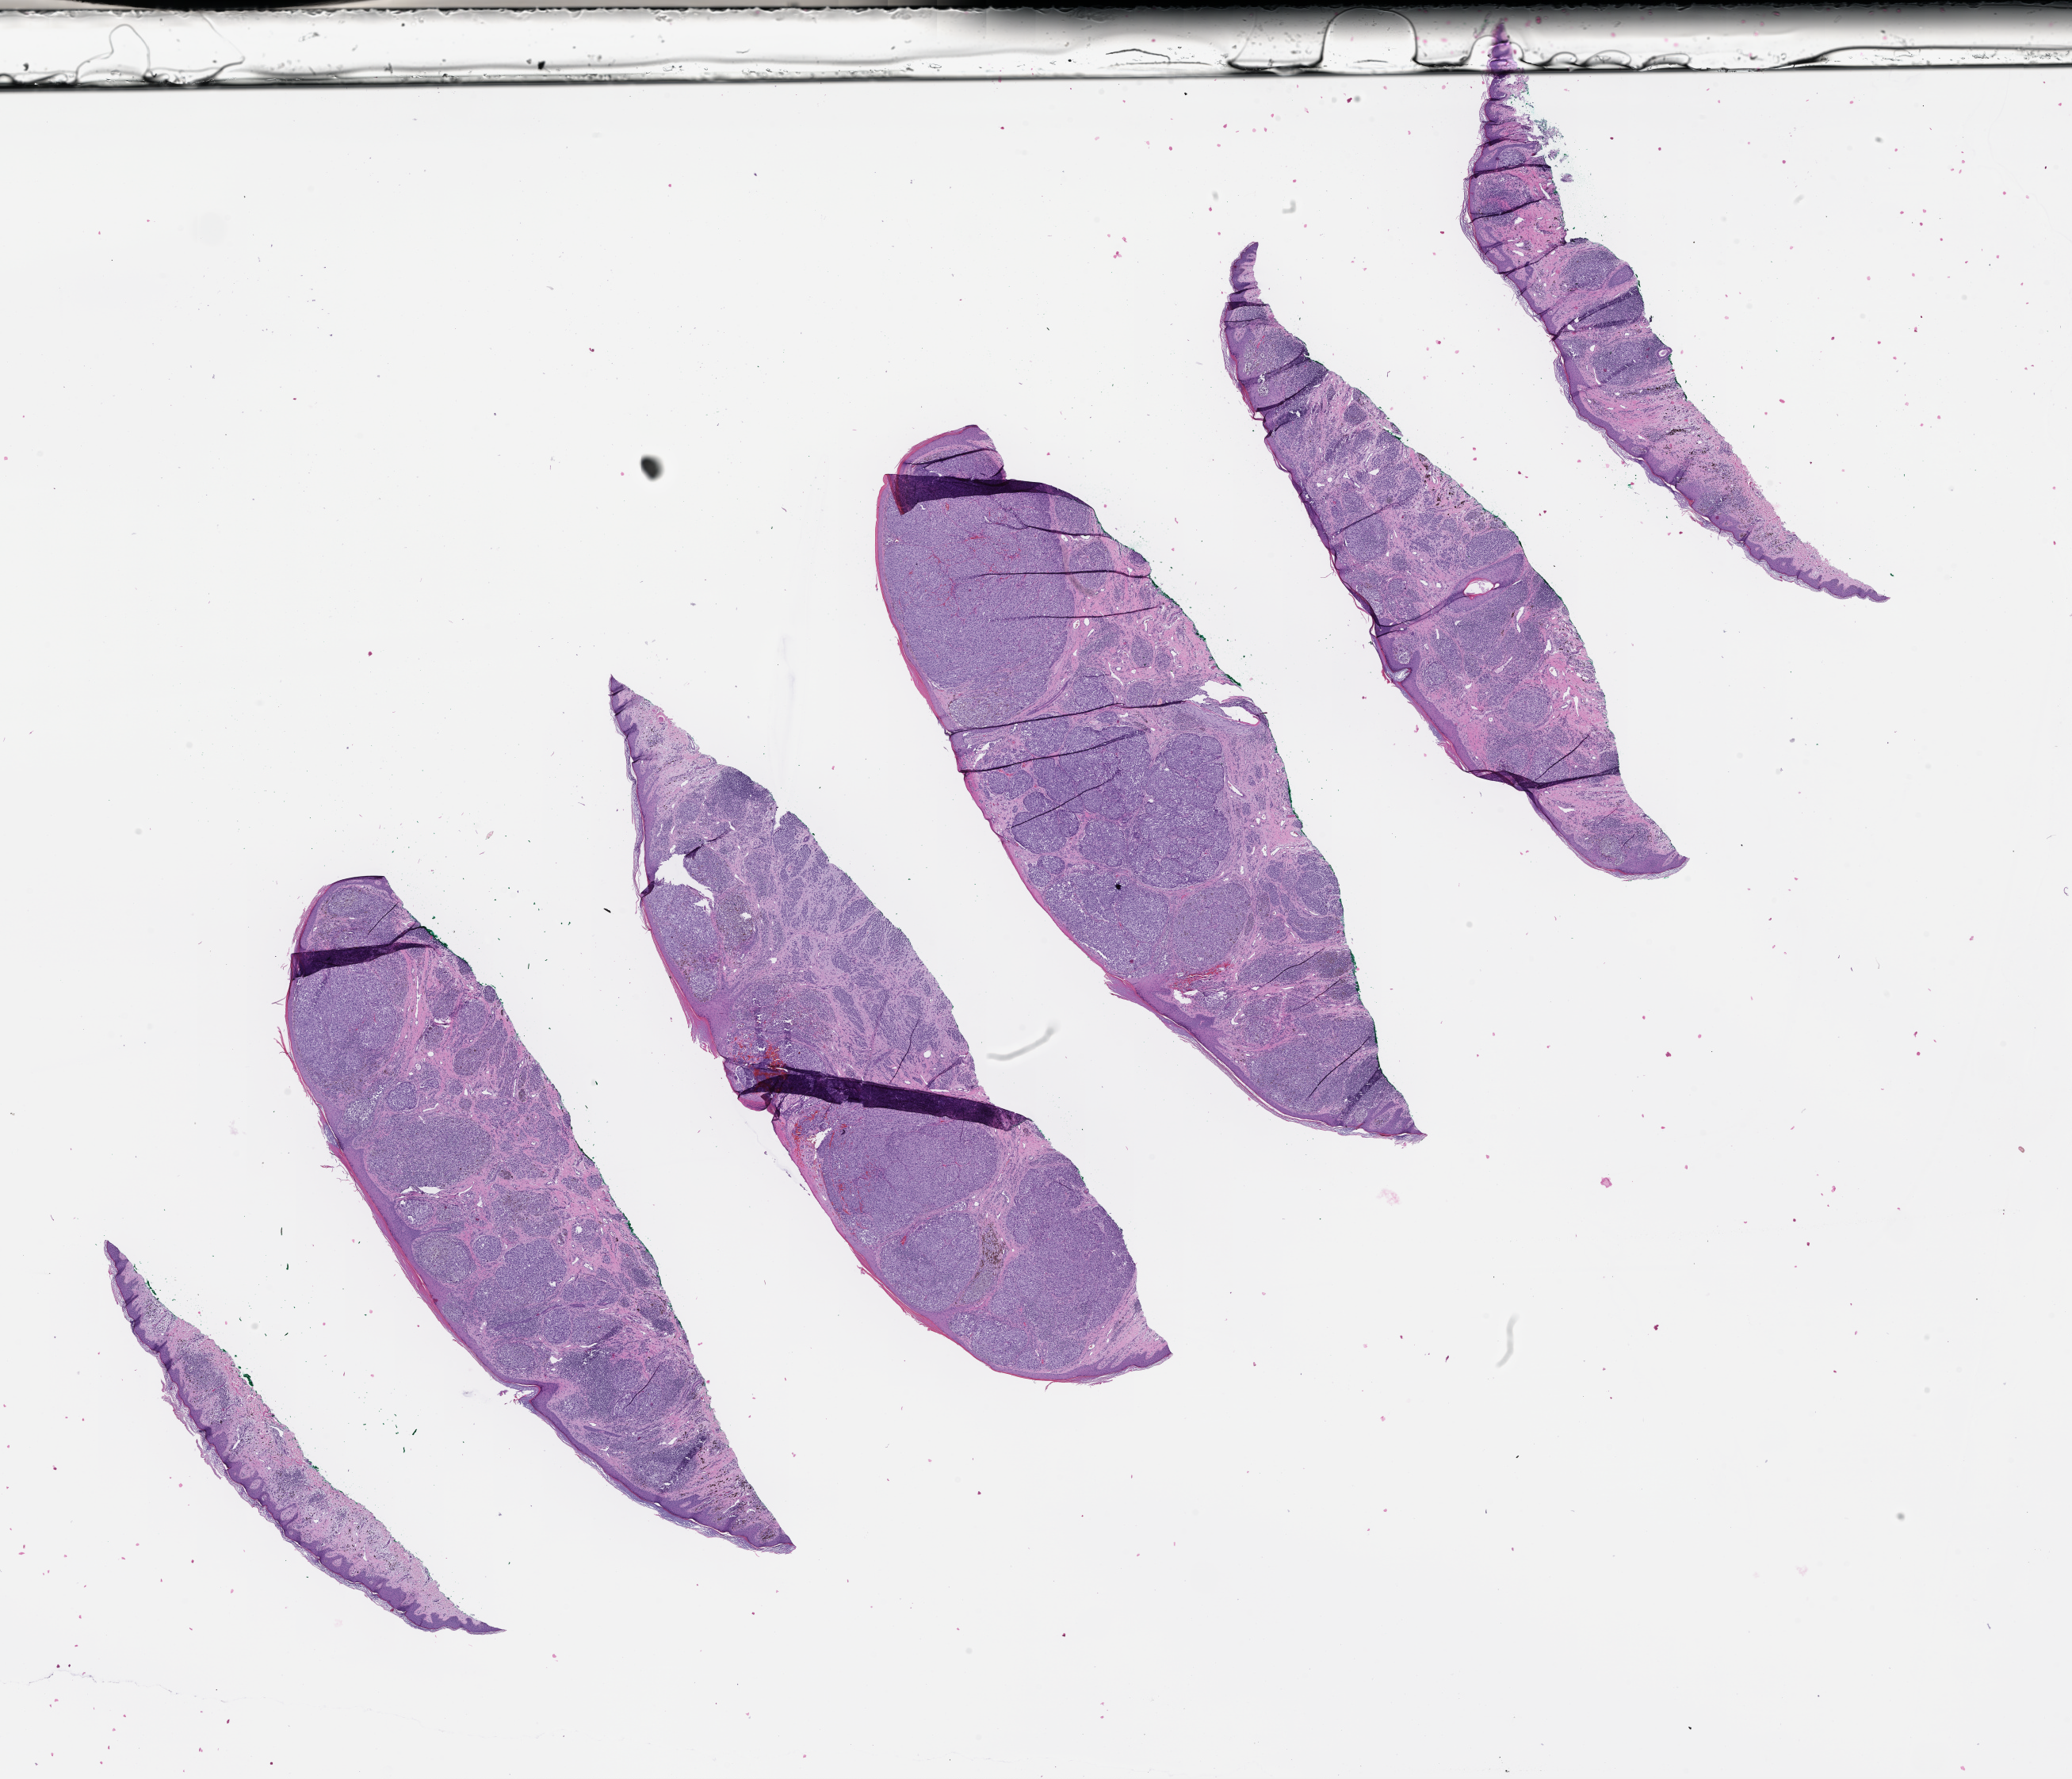
Digitized haematoxylin and eosin-stained section — low-resolution overview of the scanned area, about 21.1 x 18.1 mm; FFPE section; site: skin; specimen time point: archival tissue. Patient sex: male.
This section: primary tumor. Diagnosis: Melanoma.